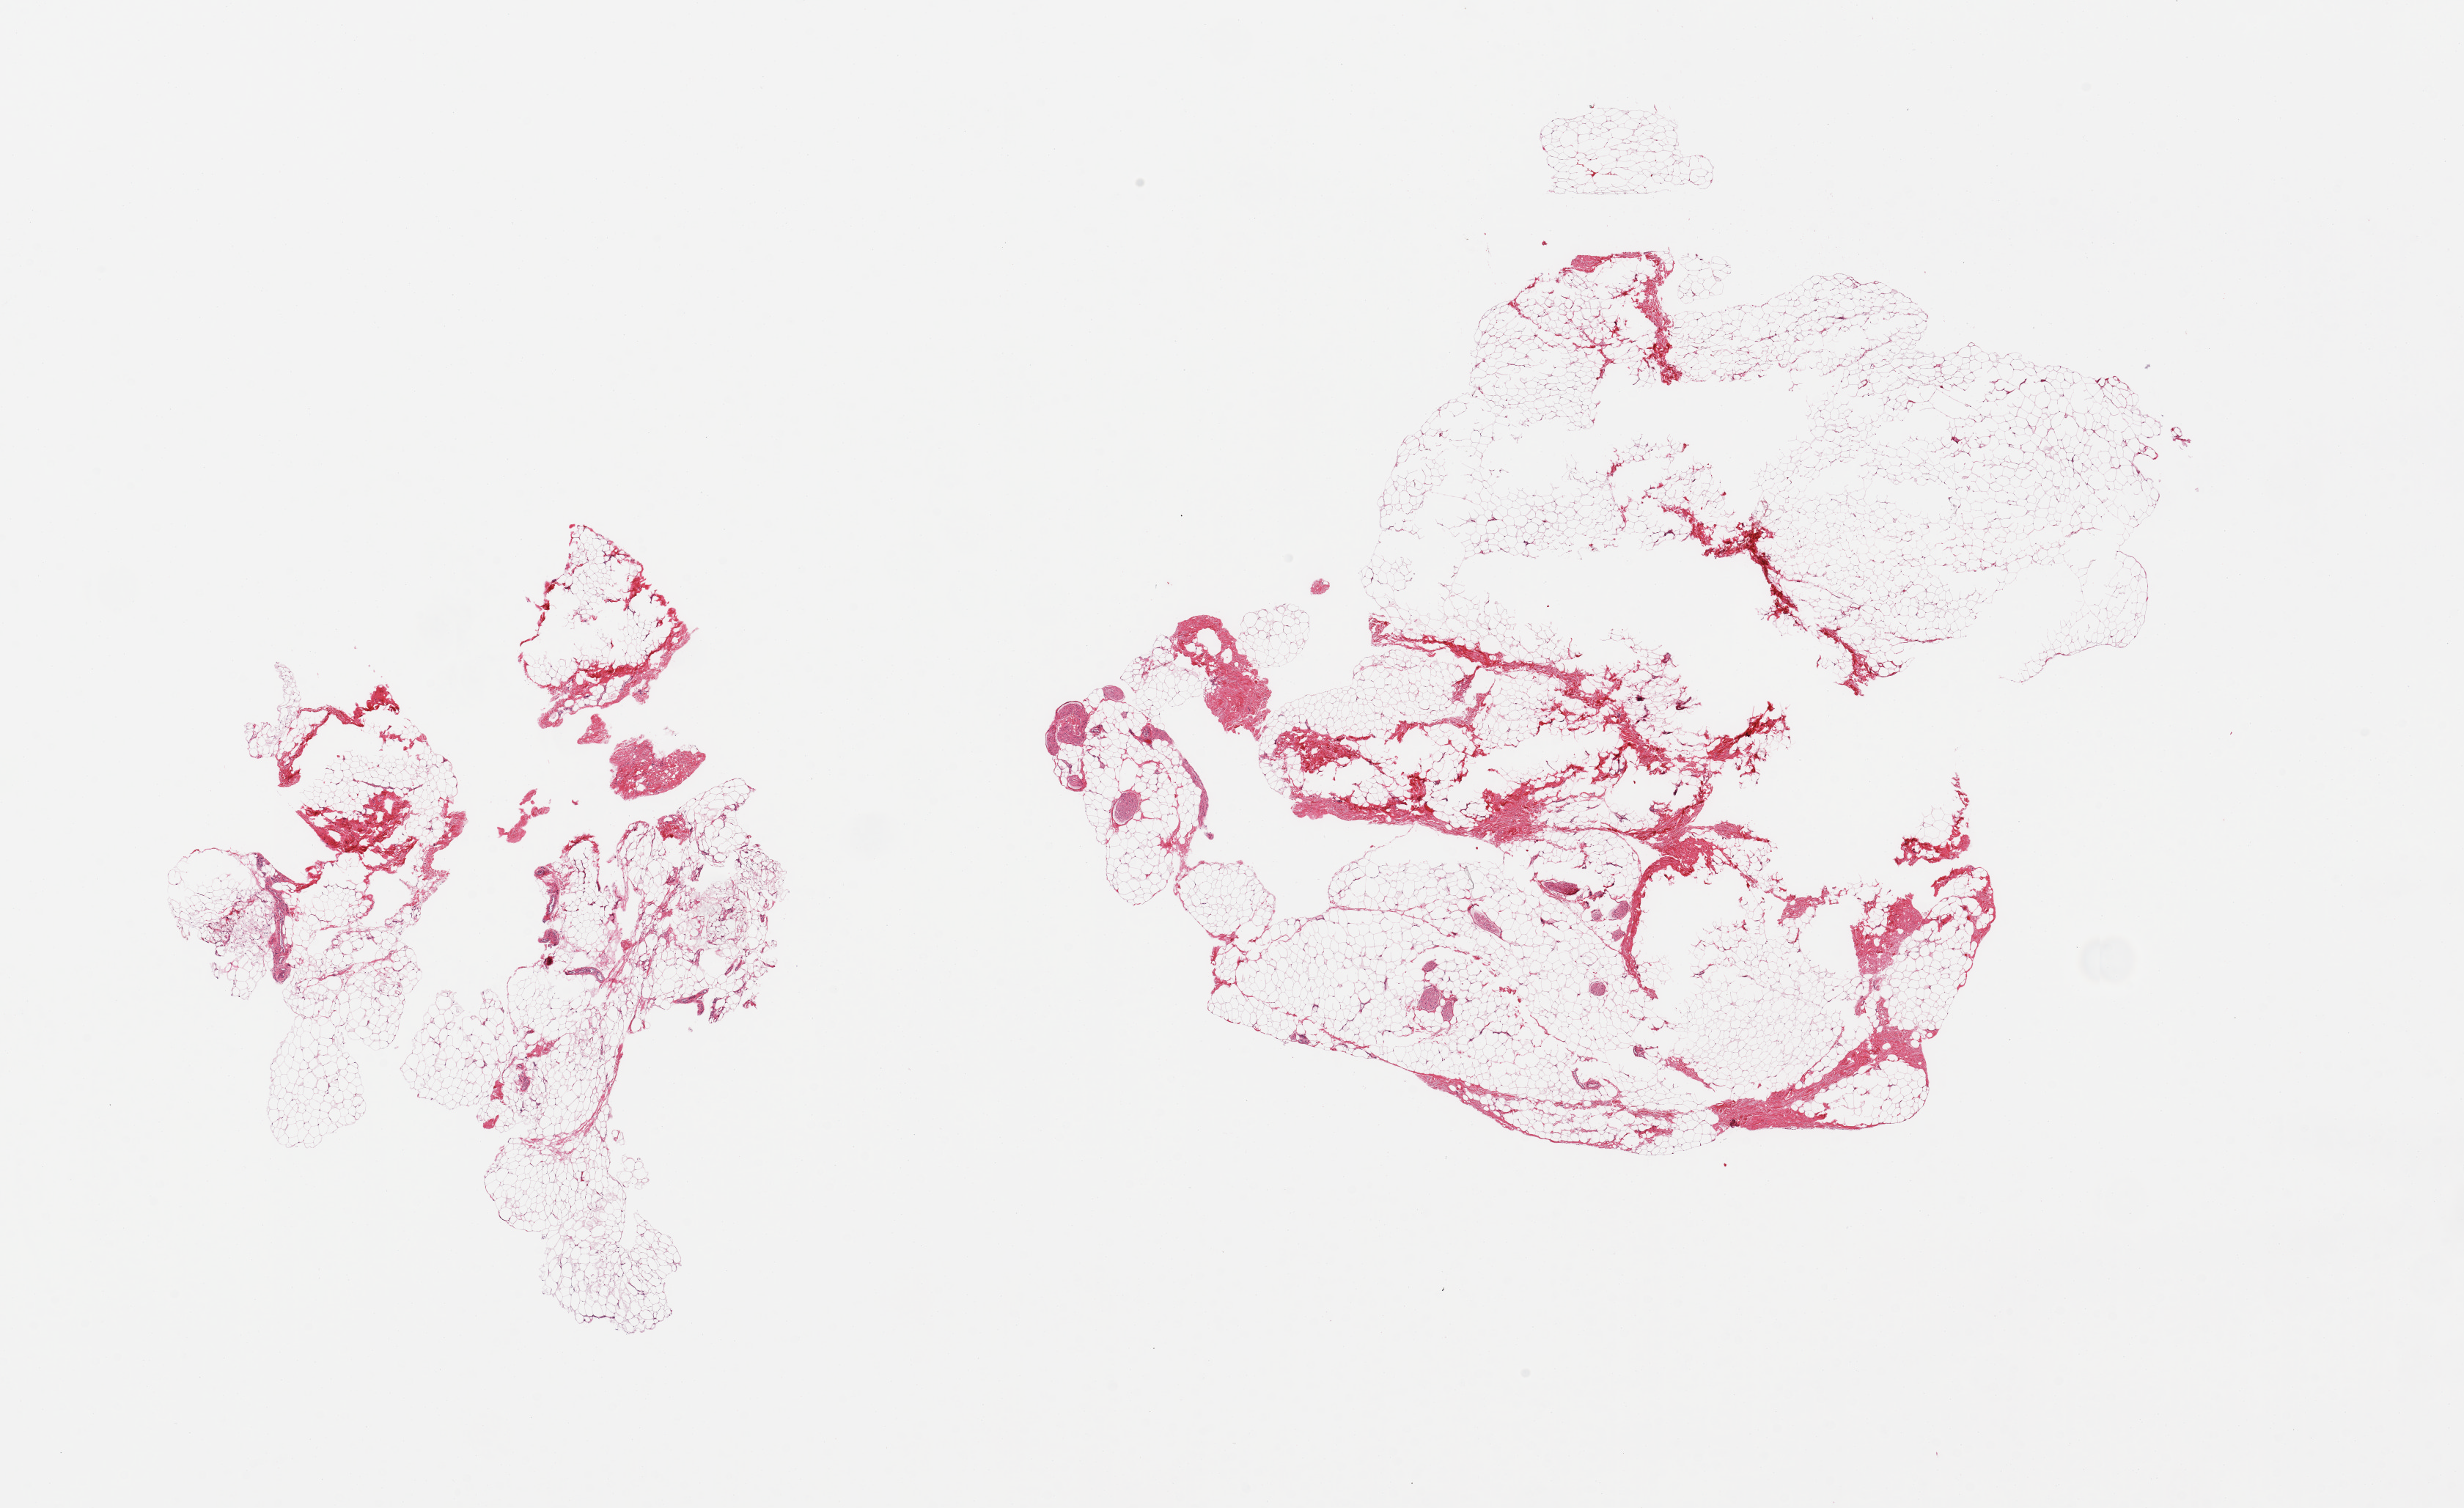
Digitized H&E-stained section, a low-resolution overview of the entire scanned area, about 26.6 x 16.3 mm; PAXgene-fixed paraffin-embedded (PFPE) section; target tissue: breast; tissue donor sample. Donor sex: male.
- reviewer comment on this tissue sample: 2 pieces; predominantly fat with scattered fibrous tissue and nerve, no ductal elements in this section